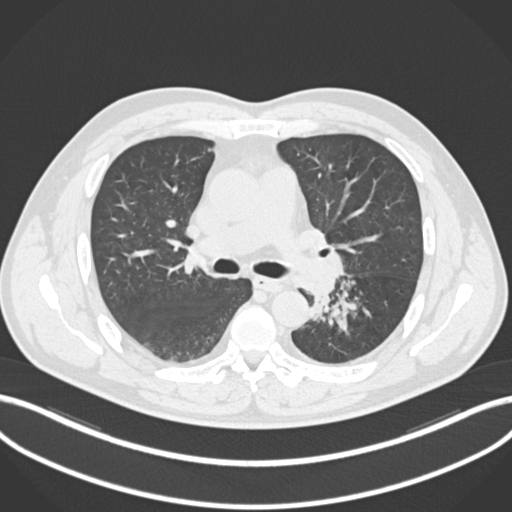
Chest CT, one axial slice. Position 138 of 223 along the scan axis. Reconstruction kernel B30f. 120 kVp. Lung window (W 1500 / L -600 HU). 1 mm slice thickness. 512 × 512 image matrix, field of view 400 × 400 mm. Patient: male, 50 years. Case-level facts recorded for this patient, not image findings: clinical TNM (as recorded): T2a N3 M0.
Outlined on this slice (rectangle marked by the reading radiologist):
- lung tumour (recorded histology: squamous cell carcinoma): bounding box <308,273,336,301> (left, top, right, bottom; pixels)